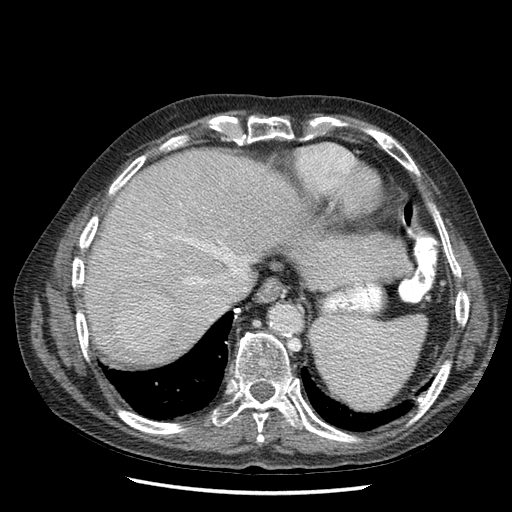
Contrast-enhanced abdominal CT (liver protocol), one axial slice; slice 52 of 67 in the series (ordered by position); reconstruction kernel STANDARD; 120 kVp; soft-tissue window (W 400 / L 40 HU); 2.5 mm slice thickness; 512 × 512 image matrix. Case-level facts recorded for this patient, not image findings: diagnosis: hepatocellular carcinoma (patient treated with transarterial chemoembolisation; whether this scan precedes or follows treatment is not stated here); TNM stage (as recorded): Stage-I; Child-Pugh class: A; tumour differentiation: moderately differentiated; tumour nodularity: uninodular.
Outlined on this slice (semi-automatic segmentation, software-assisted and operator-edited):
- liver parenchyma outside the tumour (the mass and vessels are separate outlines, so this box may not span the whole liver): bounding box [x1, y1, x2, y2] px = [84, 146, 410, 370]
- mass: [111, 288, 176, 355]
- liver vessels: [139, 204, 179, 262]